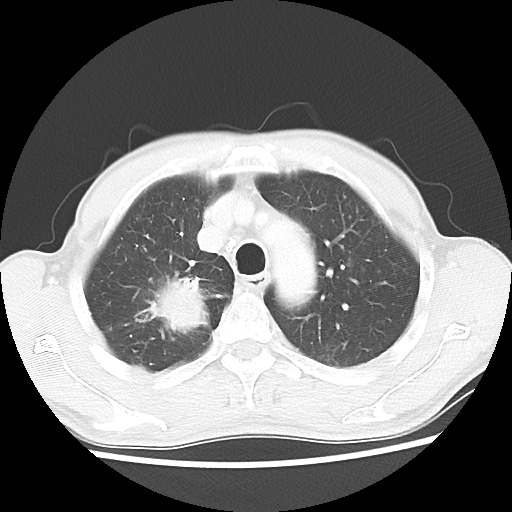
Chest CT, one axial slice; slice 41 of 52 in the series (ordered by position); lung window (W 1500 / L -600 HU); 5 mm slice thickness; 512 × 512 image matrix. Patient: male, 66 years. Case-level facts recorded for this patient, not image findings: clinical TNM (as recorded): T2 N0 M1a.
Annotated regions visible in this slice (bounding box drawn by a radiologist):
- lung tumour (recorded histology: adenocarcinoma): bounding box [x1, y1, x2, y2] px = [138, 270, 220, 335]